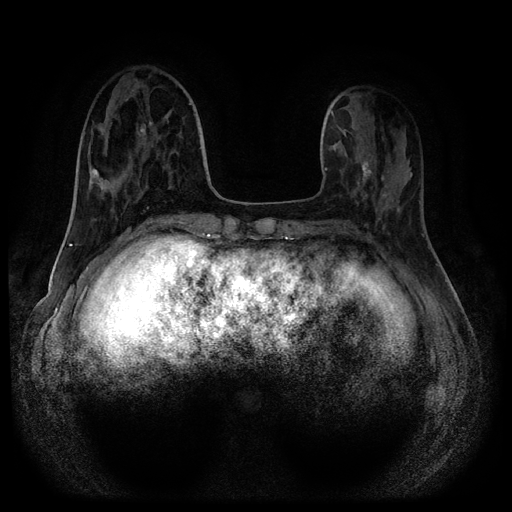
Breast MRI (dynamic contrast-enhanced, multi-phase), one axial slice. Slice 35 of 116 in the series (ordered by position). Dynamic contrast-enhanced series, time point 2 of 5 at this slice position (early post-contrast). 1.5 T. TE 2.7 ms, TR 5.4 ms. 512 × 512 image matrix, field of view 340 × 340 mm. Patient: female, 40 years.
Annotated regions visible in this slice (semi-automatic segmentation, software-assisted and operator-edited):
- breast lesion (labelled benign in the annotation): bounding box [x1, y1, x2, y2] px = [350, 155, 374, 195]